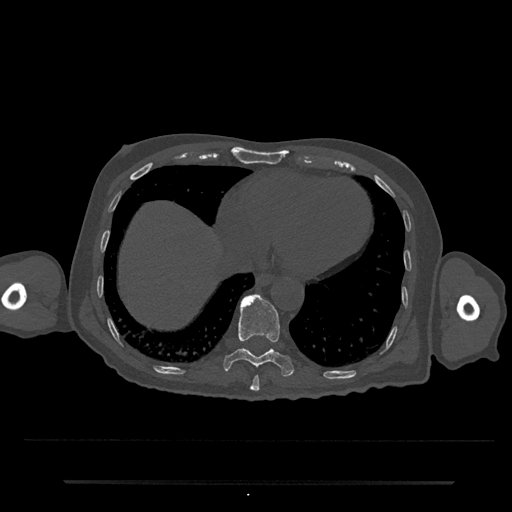
CT including the spine, one axial slice. Slice 315 of 797 in the series (ordered by position). 120 kVp. Bone window (W 1800 / L 400 HU). 0.5 mm slice thickness. 512 × 512 image matrix, field of view 427 × 427 mm. Patient: male, 74 years. From the clinical record (not read from this slice): primary cancer: prostate.
Outlined on this slice (semi-automatically segmented with operator editing):
- T10 vertebra: bounding box [x1, y1, x2, y2] px = [223, 294, 294, 377]
- T9 vertebra: [250, 375, 260, 392]